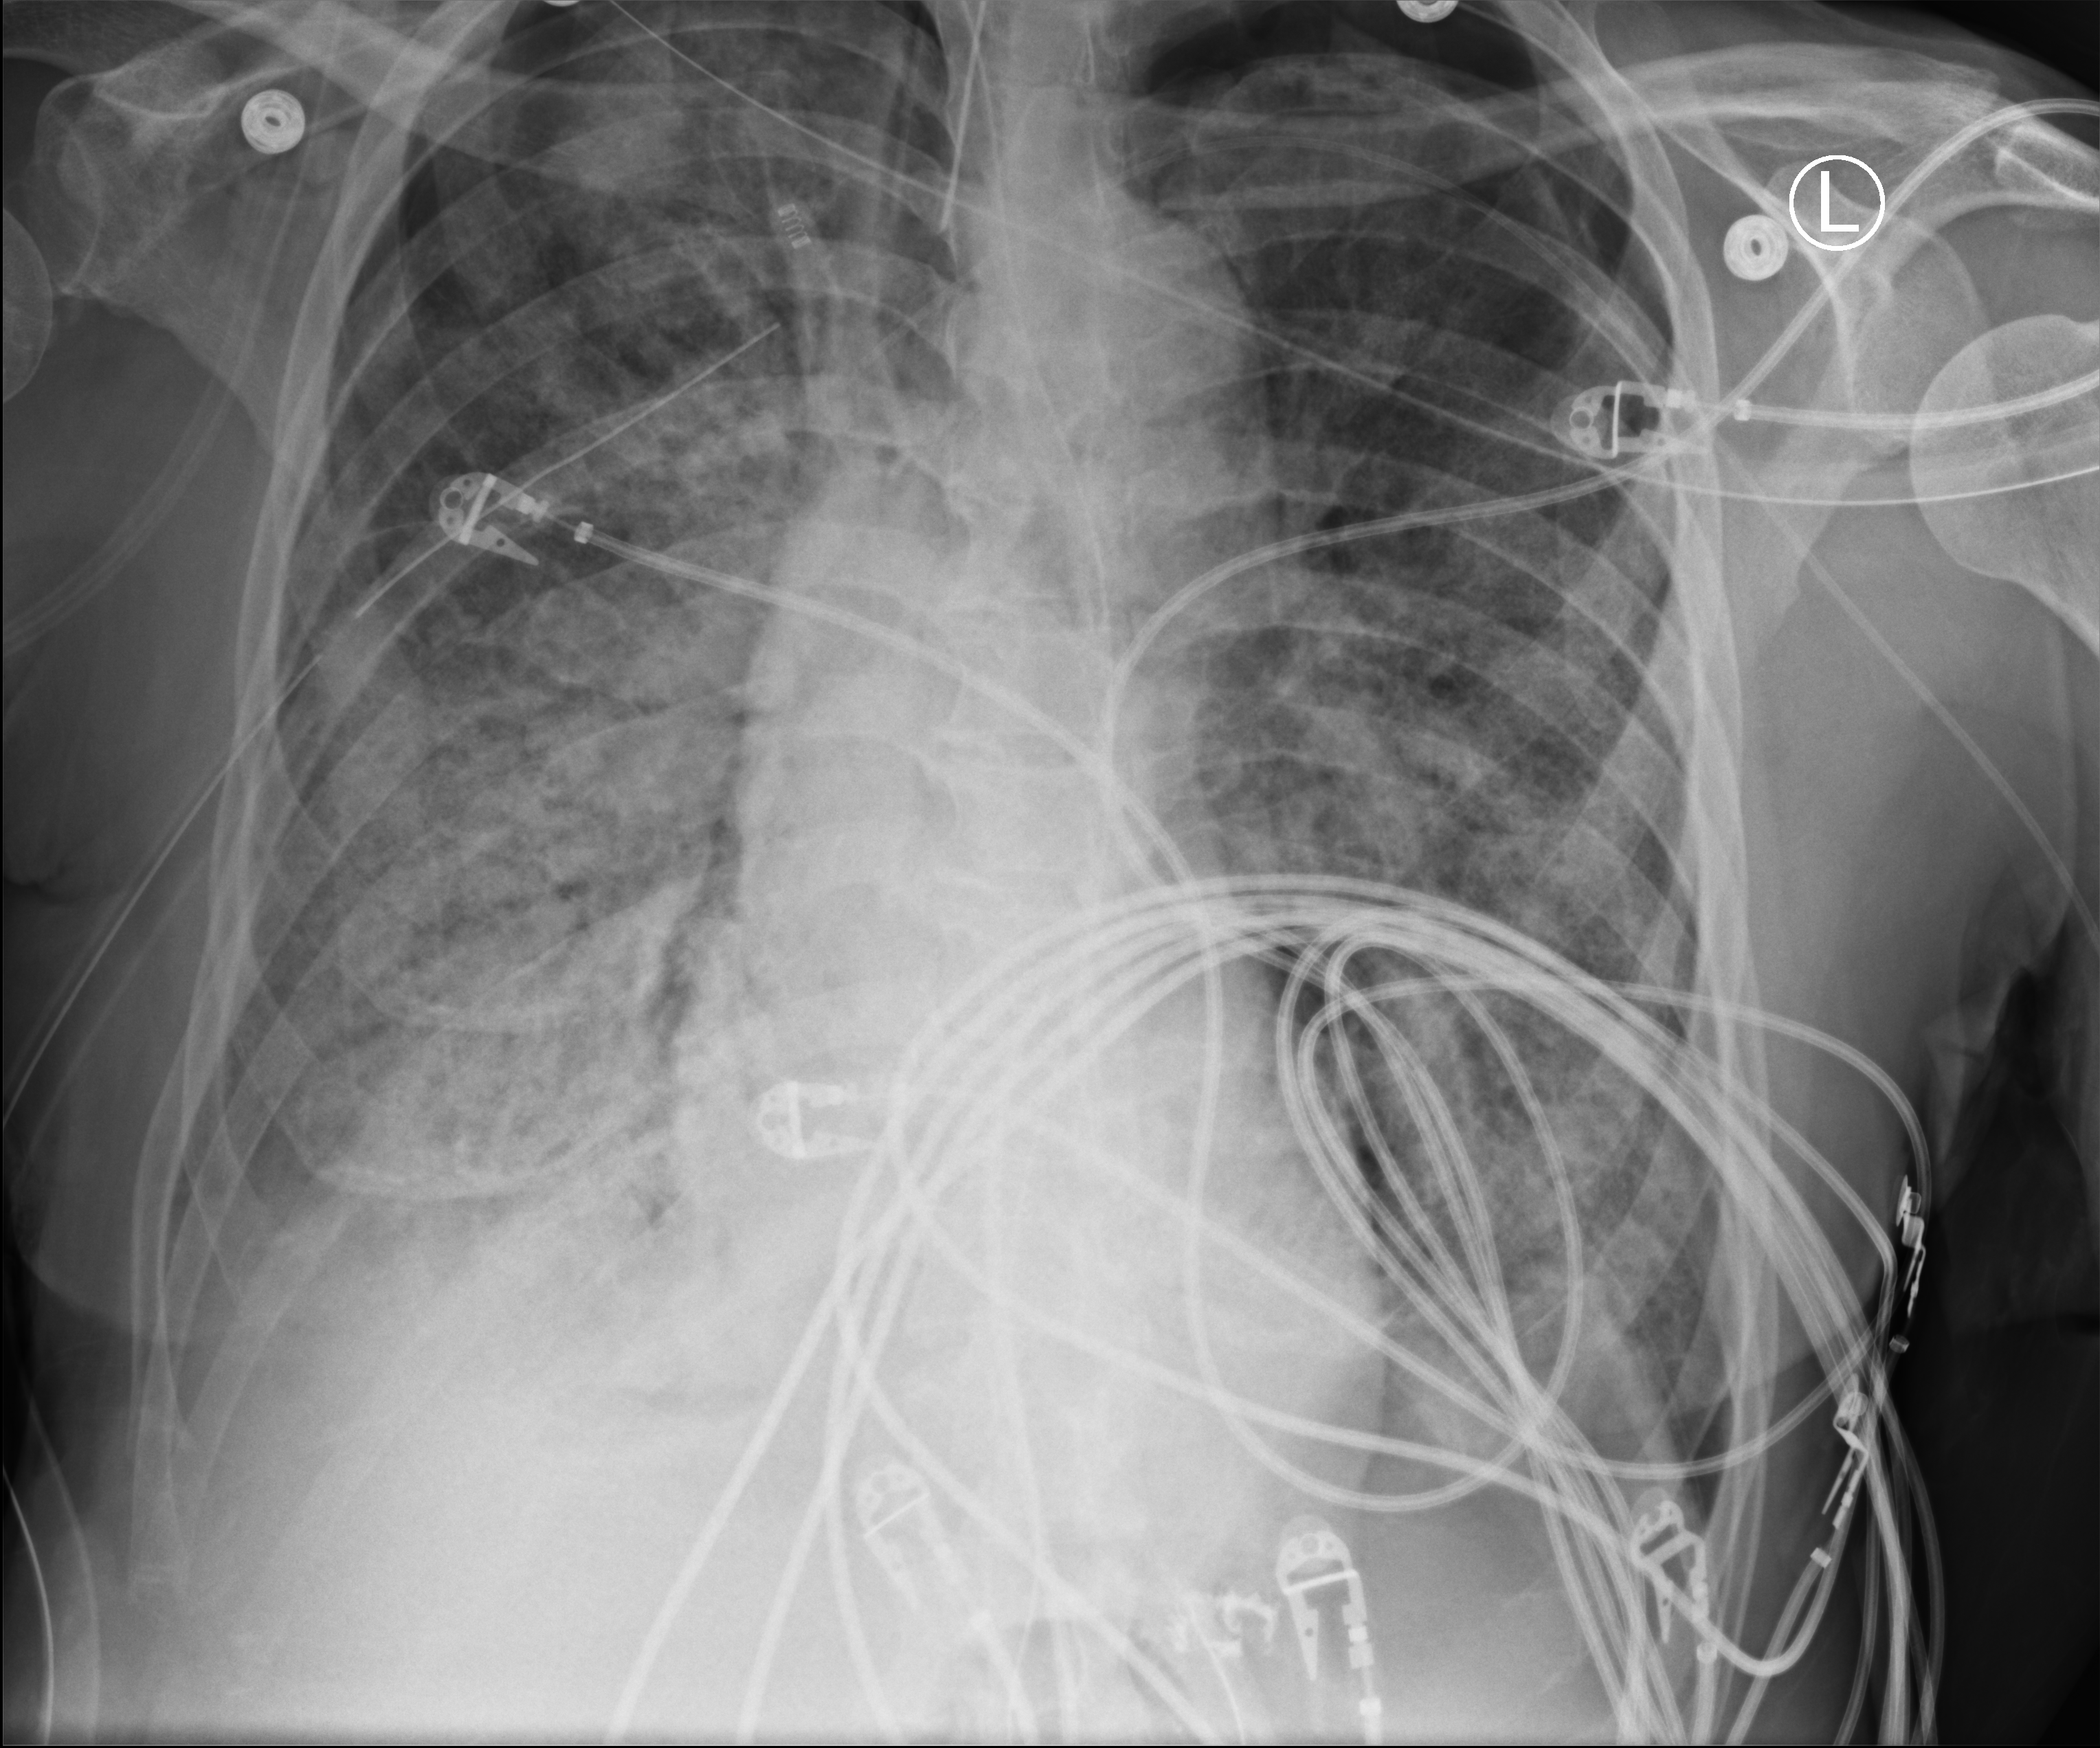
Portable chest radiograph; anteroposterior (AP) projection. Male patient hospitalised with COVID-19, age 60–74 years.
From the hospital-stay record, not from the radiograph (when in the stay this image was taken is not recorded): smoking status (admission record): former; hypertension (admission record): no; admitted to intensive care during this hospital stay: yes.